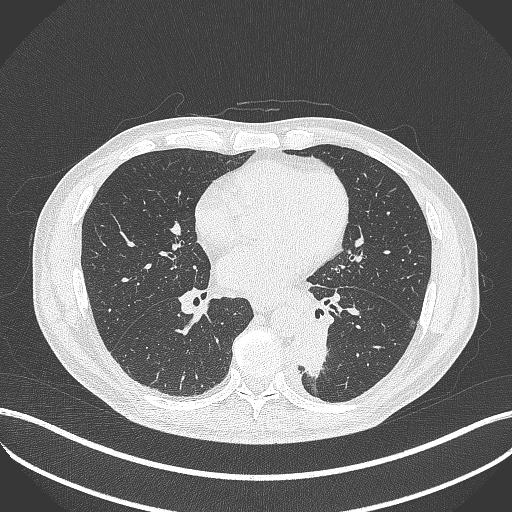
Chest CT, one axial slice. Position 186 of 451 along the scan axis. 120 kVp. Lung window (W 1500 / L -600 HU). 1 mm slice thickness. 512 × 512 image matrix, field of view 400 × 400 mm. Patient: male, 72 years. Case-level facts recorded for this patient, not image findings: clinical TNM (as recorded): T2b N0 M1.
Structures marked on this image (bounding box drawn by a radiologist):
- lung tumour (recorded histology: adenocarcinoma): bounding box [x1, y1, x2, y2] px = [296, 314, 331, 381]